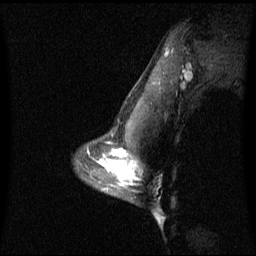
Breast MRI (dynamic contrast-enhanced), one sagittal slice; slice 48 of 60 in the series (ordered by position); dynamic contrast-enhanced series, image 2 of 3 at this slice position (ordered by acquisition); 1.5 T; TE 4.2 ms, TR 8.4 ms; 2.3 mm slice thickness; 256 × 256 image matrix. Female patient, age 42 years. Case-level facts recorded for this patient, not image findings: setting: breast cancer imaged before/during neoadjuvant chemotherapy; receptor status: triple-negative.
Outlined on this slice (semi-automatic segmentation, software-assisted and operator-edited):
- analysis volume of interest (the breast-tissue region the enhancement analysis was run in; not a lesion): bounding box <106,156,134,187> (left, top, right, bottom; pixels)
- tumour enhancement mask (voxels above the 70 % enhancement threshold inside the analysis volume of interest): <119,164,134,185>